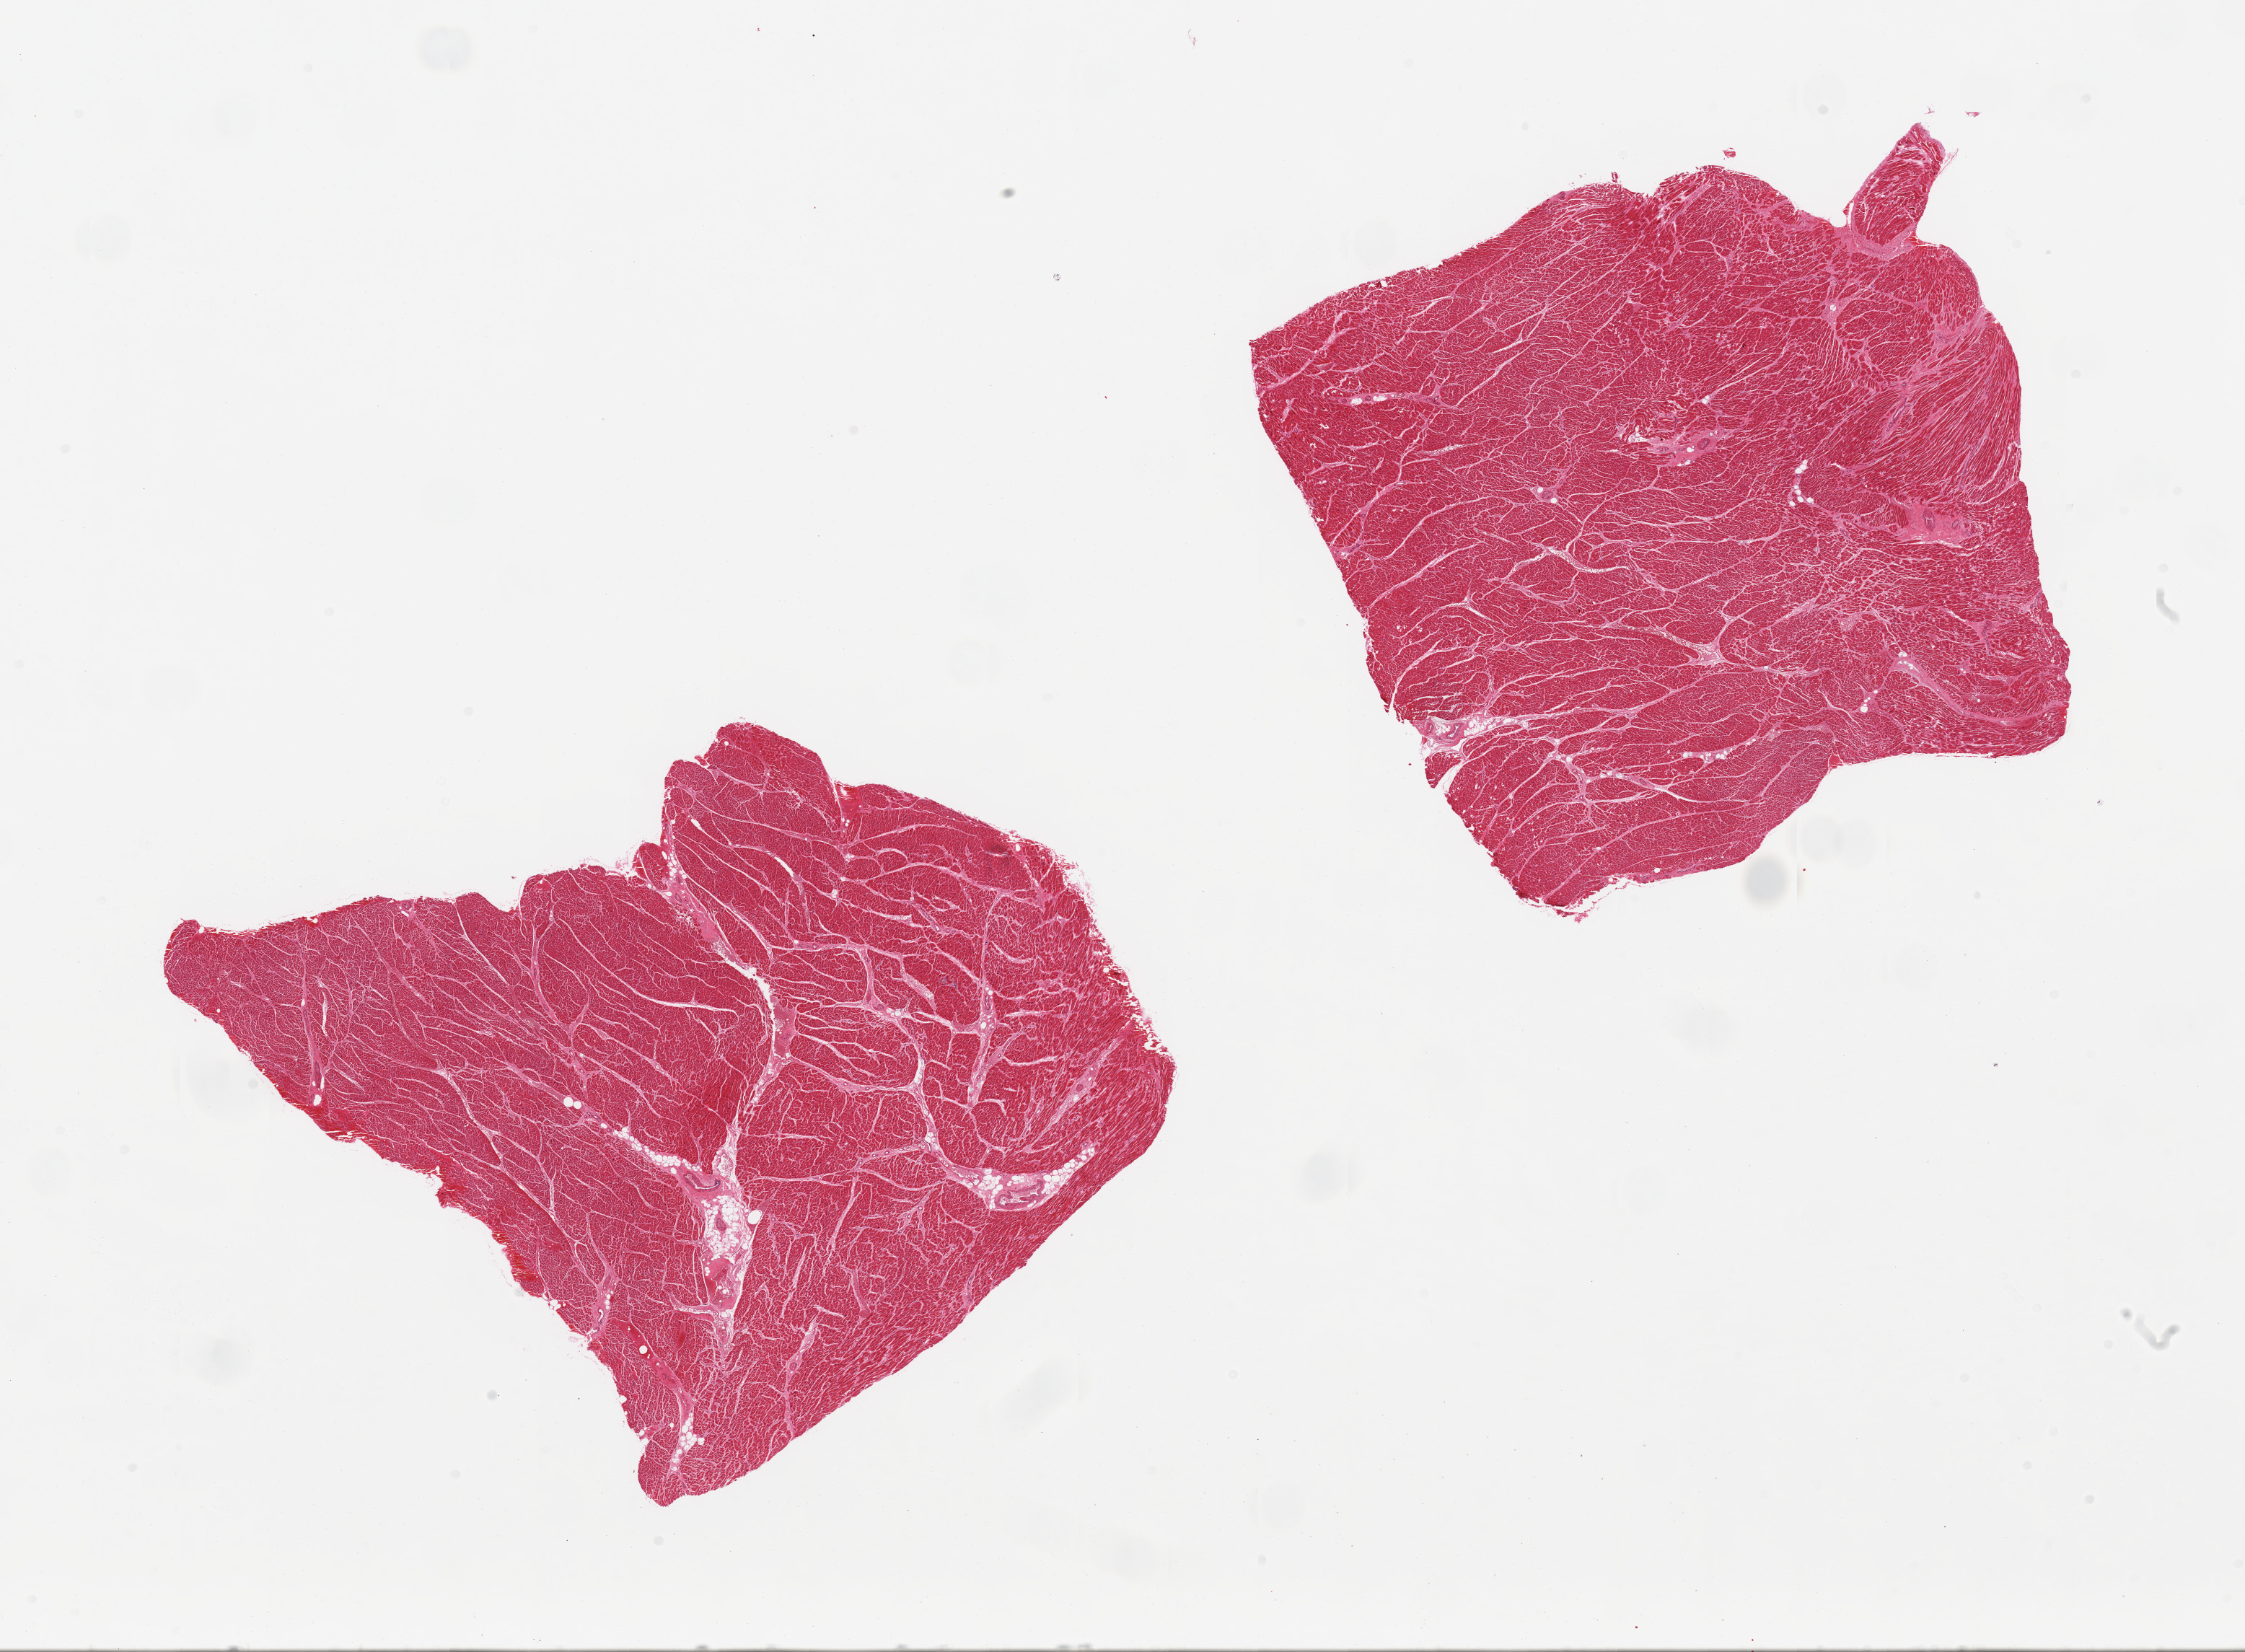
Digitized hematoxylin and eosin (H&E)-stained section, brightfield, shown as a low-resolution overview of the whole scanned area (about 24.6 x 18.1 mm); PAXgene-fixed paraffin-embedded (PFPE) section; target tissue: heart; tissue donor sample. Male donor.
Review note (as recorded): 2 pieces, interstitial/focal patchy fibrosis.